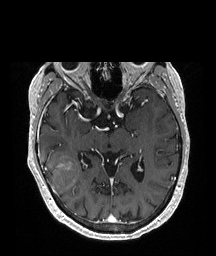
Brain MRI from a brain-tumour surgery series, one axial slice; slice 120 of 208 in the series (ordered by position); T1-weighted post-contrast; 1 mm slice thickness; 216 × 256 image matrix, field of view 216 × 256 mm. Case-level facts recorded for this patient, not image findings: histopathology: Glioblastoma; WHO grade: 4; IDH mutation: no.
Structures marked on this image (outlined manually by an expert reader):
- tumour: box from (x=39, y=150) to (x=78, y=195) px